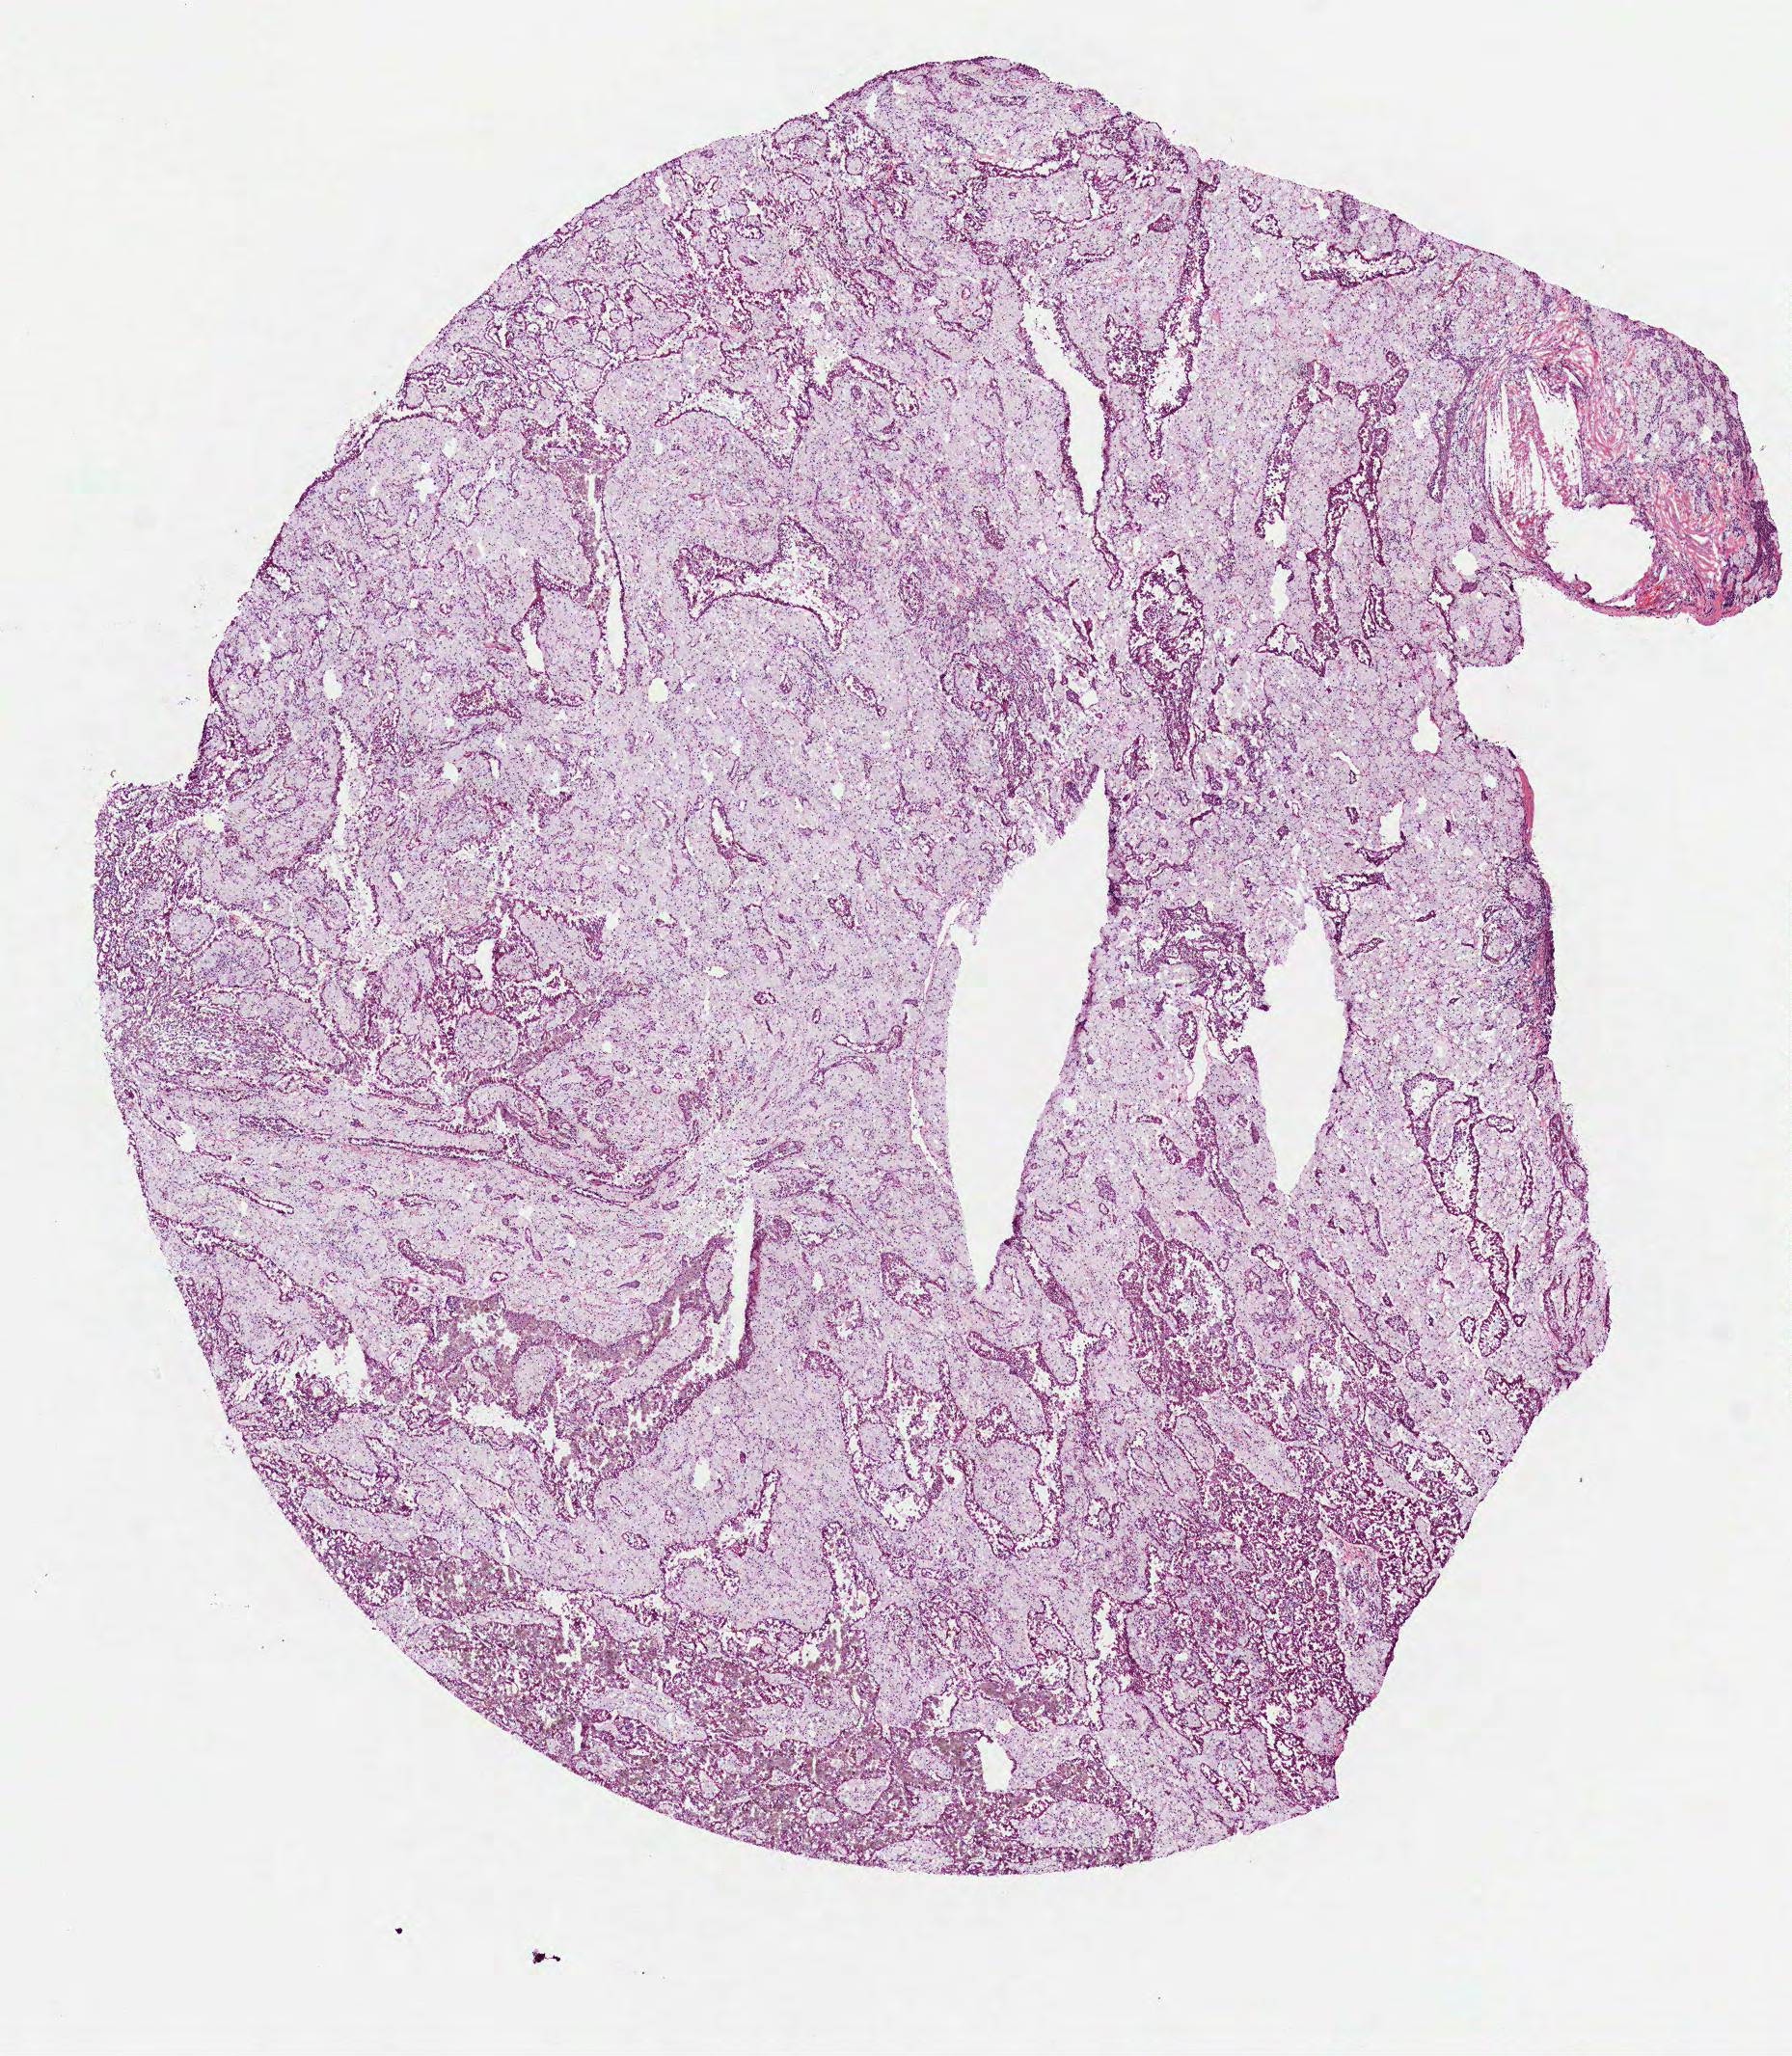
Whole-slide histology image, Hematoxylin and eosin (H&E) stained — whole scanned area (about 7.5 x 8.6 mm, from a 40x scan) shown as a low-resolution overview, frozen section from the bottom of the tissue portion, kidney, primary tumour sample. Male patient. Composition of this section per pathologist review: tumour cells 100%, tumour nuclei 60%, normal cells 0%, stromal cells 0%, necrosis 0%. Infiltration values recorded for this section: lymphocyte infiltration 2%, monocyte infiltration 30%, neutrophil infiltration 0%.
AJCC pathologic stage: I (6th edition). Pathologic diagnosis: Papillary adenocarcinoma, NOS.